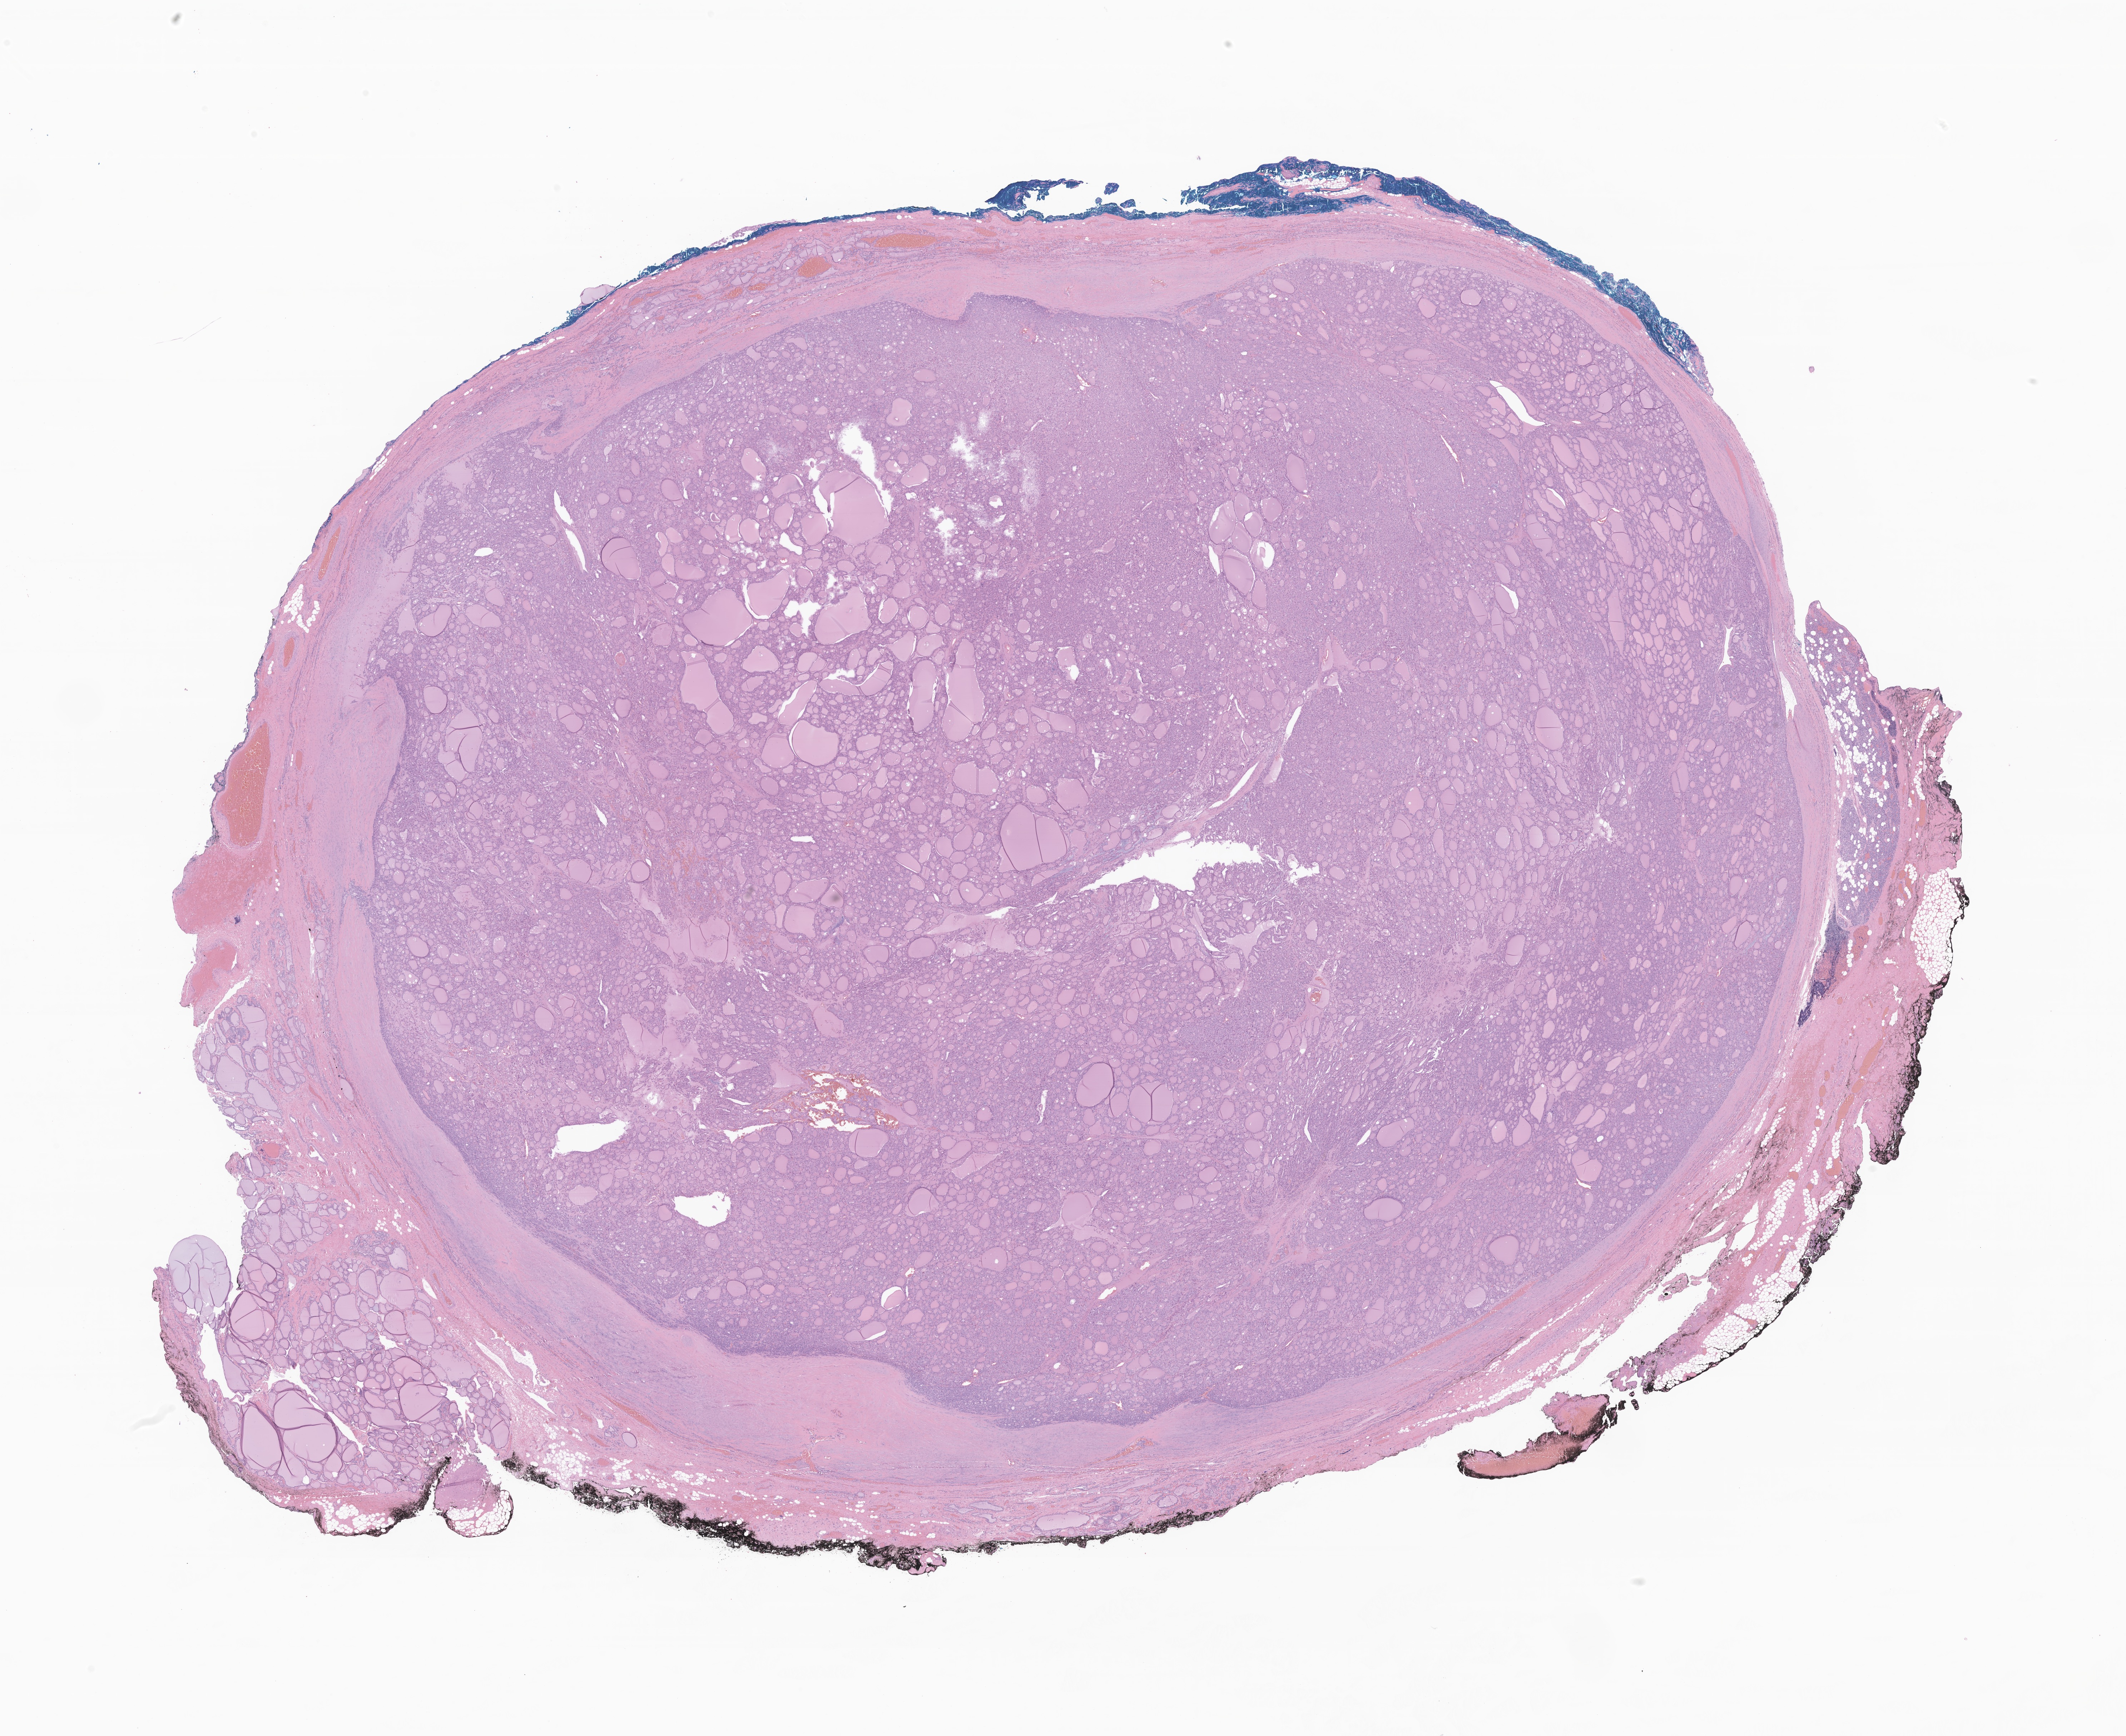
Digitized H&E-stained section of tumor tissue from the thyroid, low-resolution overview of the scanned area, about 25.1 x 20.5 mm, formalin-fixed paraffin-embedded section. Female patient, age 221 months.
• recorded diagnosis: Papillary carcinoma, follicular variant